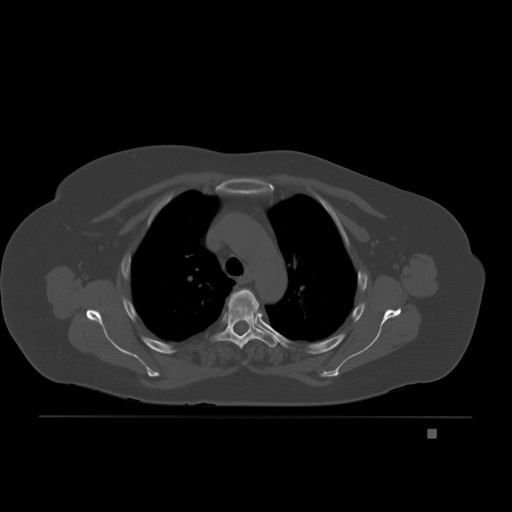
CT including the spine, one axial slice. Slice 154 of 221 in the series (ordered by position). Bone window (W 1800 / L 400 HU). 3 mm slice thickness. 512 × 512 image matrix. Female patient, age 63 years. Case-level facts recorded for this patient, not image findings: primary cancer: breast.
Structures marked on this image (semi-automatic segmentation, software-assisted and operator-edited):
- T3 vertebra: bounding box (x1, y1, x2, y2) in pixels: (232, 290, 257, 311)
- T4 vertebra: (212, 288, 278, 349)